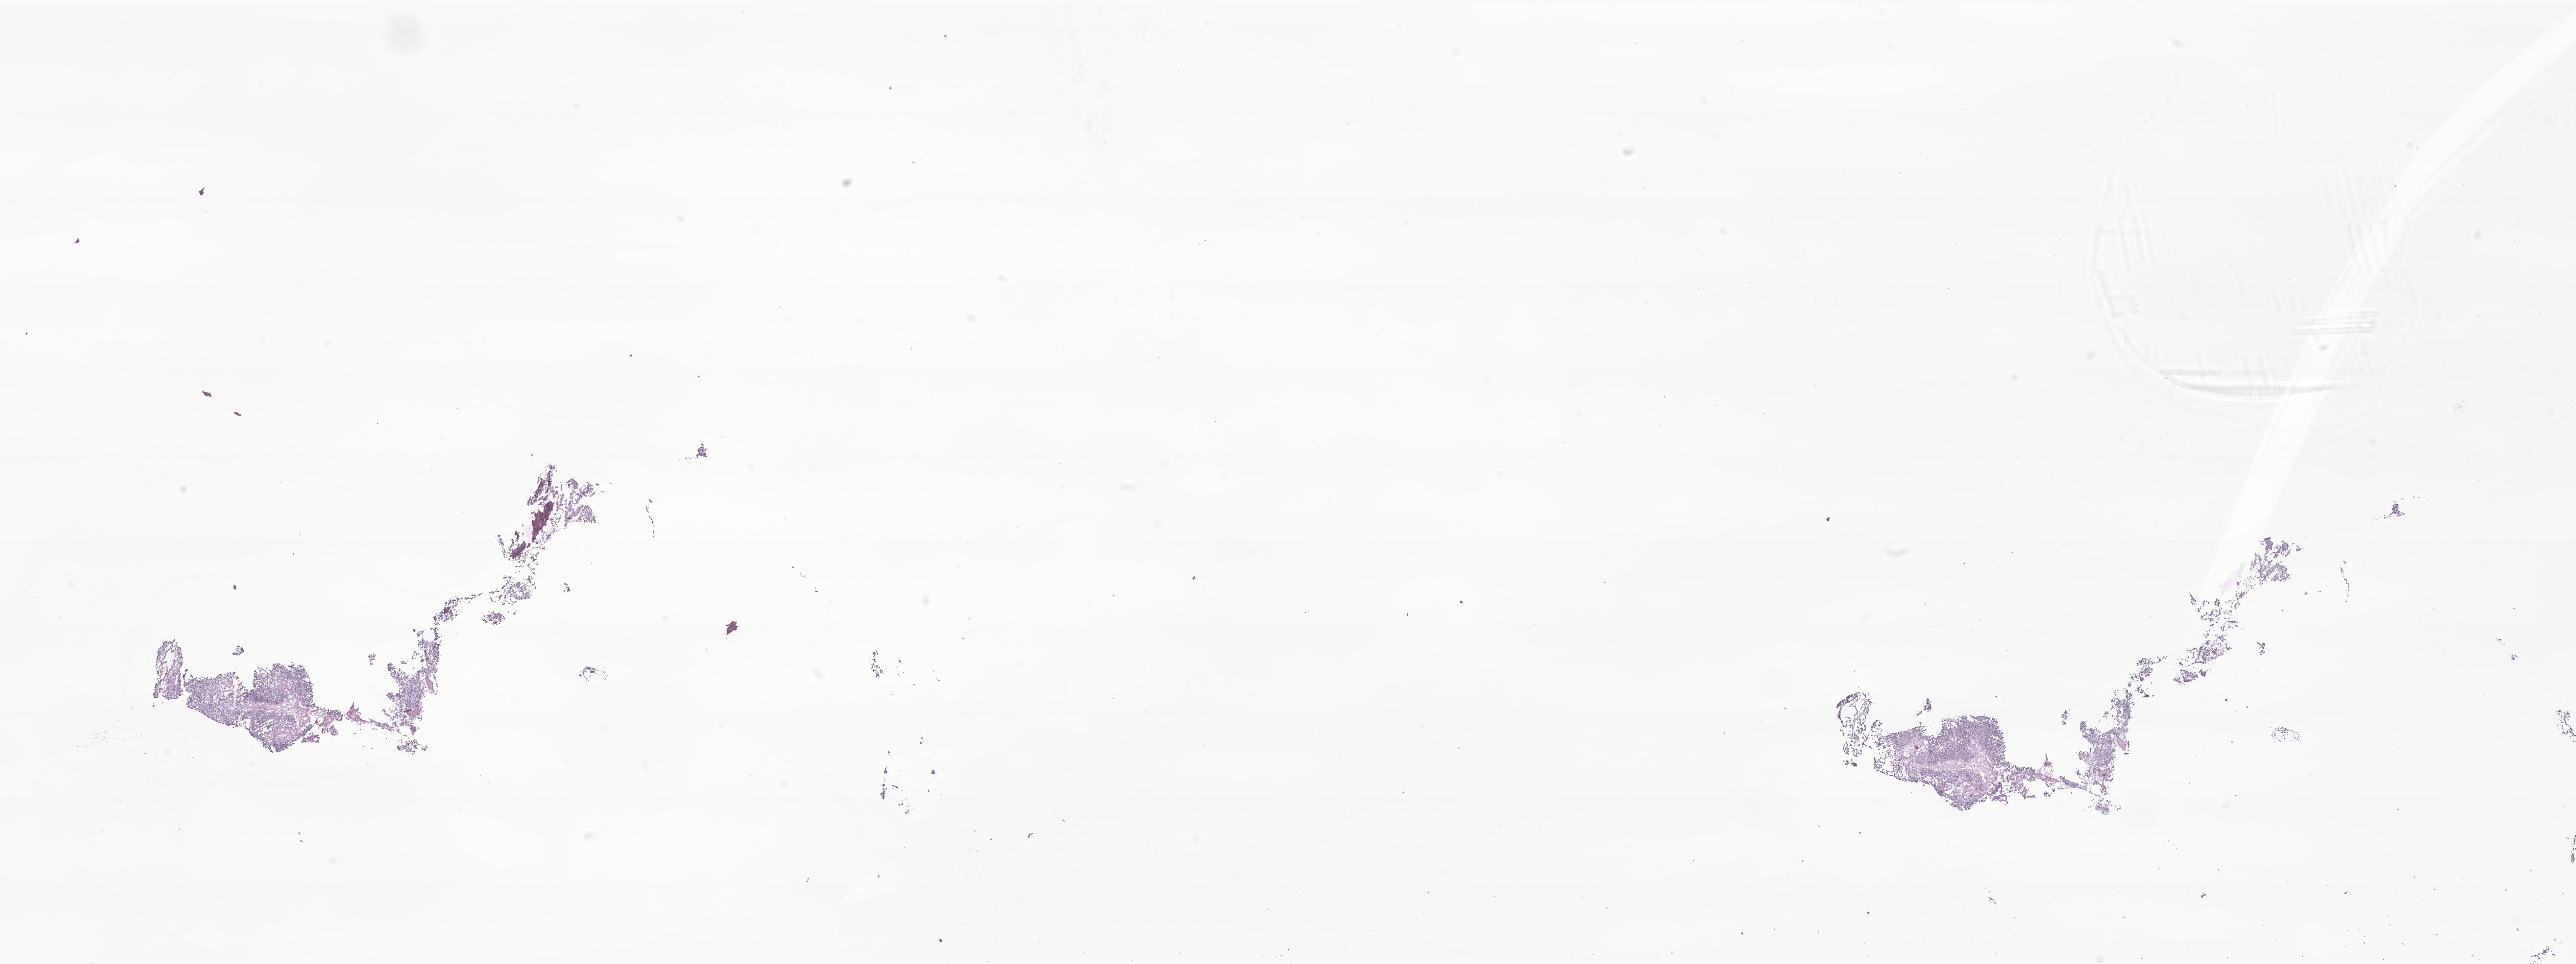
H&E whole-slide image of tumor tissue from the brain — whole scanned area (about 32.1 x 12.0 mm) shown as a low-resolution overview. Cryosection (OCT / tissue freezing medium). Patient male; age 62 months (5 years 2 months).
Diagnosis (ICD-O-3 morphology term): Neoplasm, uncertain whether benign or malignant.